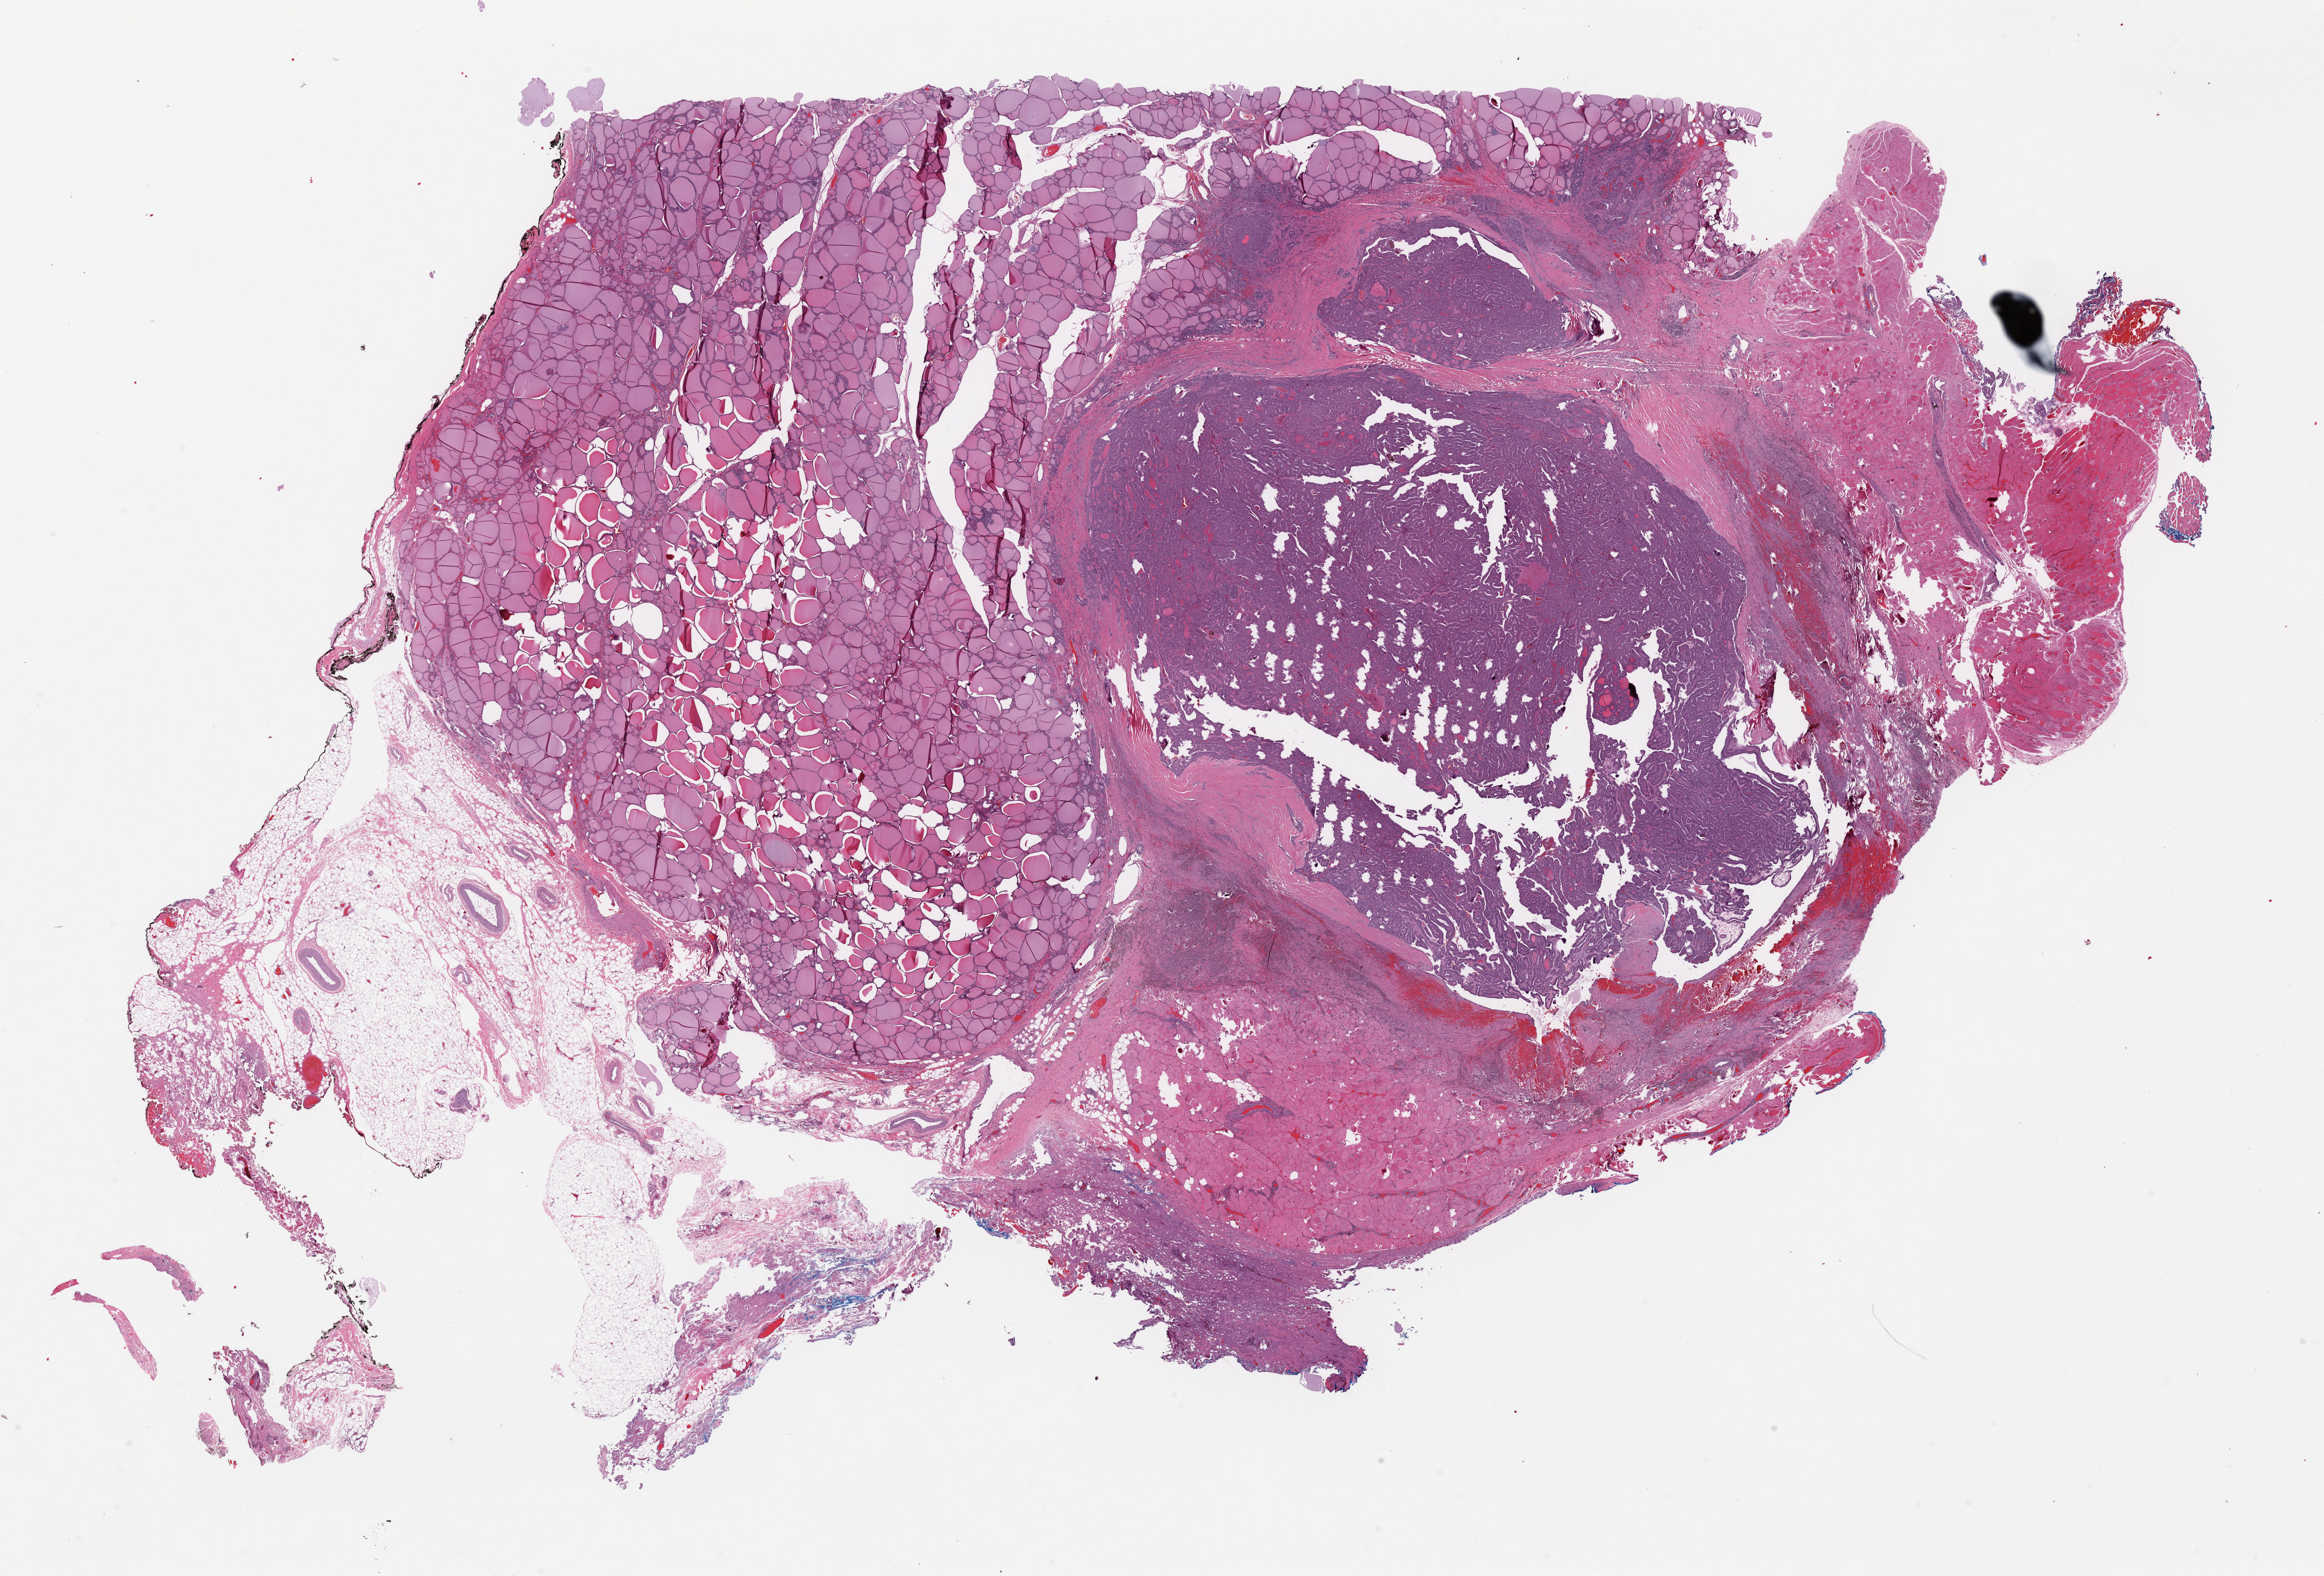
Whole-slide histology image, H&E-stained, shown as a low-resolution overview of the whole scanned area (about 31.0 x 21.0 mm, acquisition: 40x scan), formalin-fixed paraffin-embedded (FFPE) diagnostic section, sample: primary tumour, thyroid. Patient: female, age at initial diagnosis 44 years.
• TNM: T3 N0 M0
• pathologic diagnosis: Papillary carcinoma, columnar cell (thyroid gland)
• laterality: right
• lymph nodes positive (case pathology): 0 of 2 examined
• AJCC pathologic stage: III (7th edition)